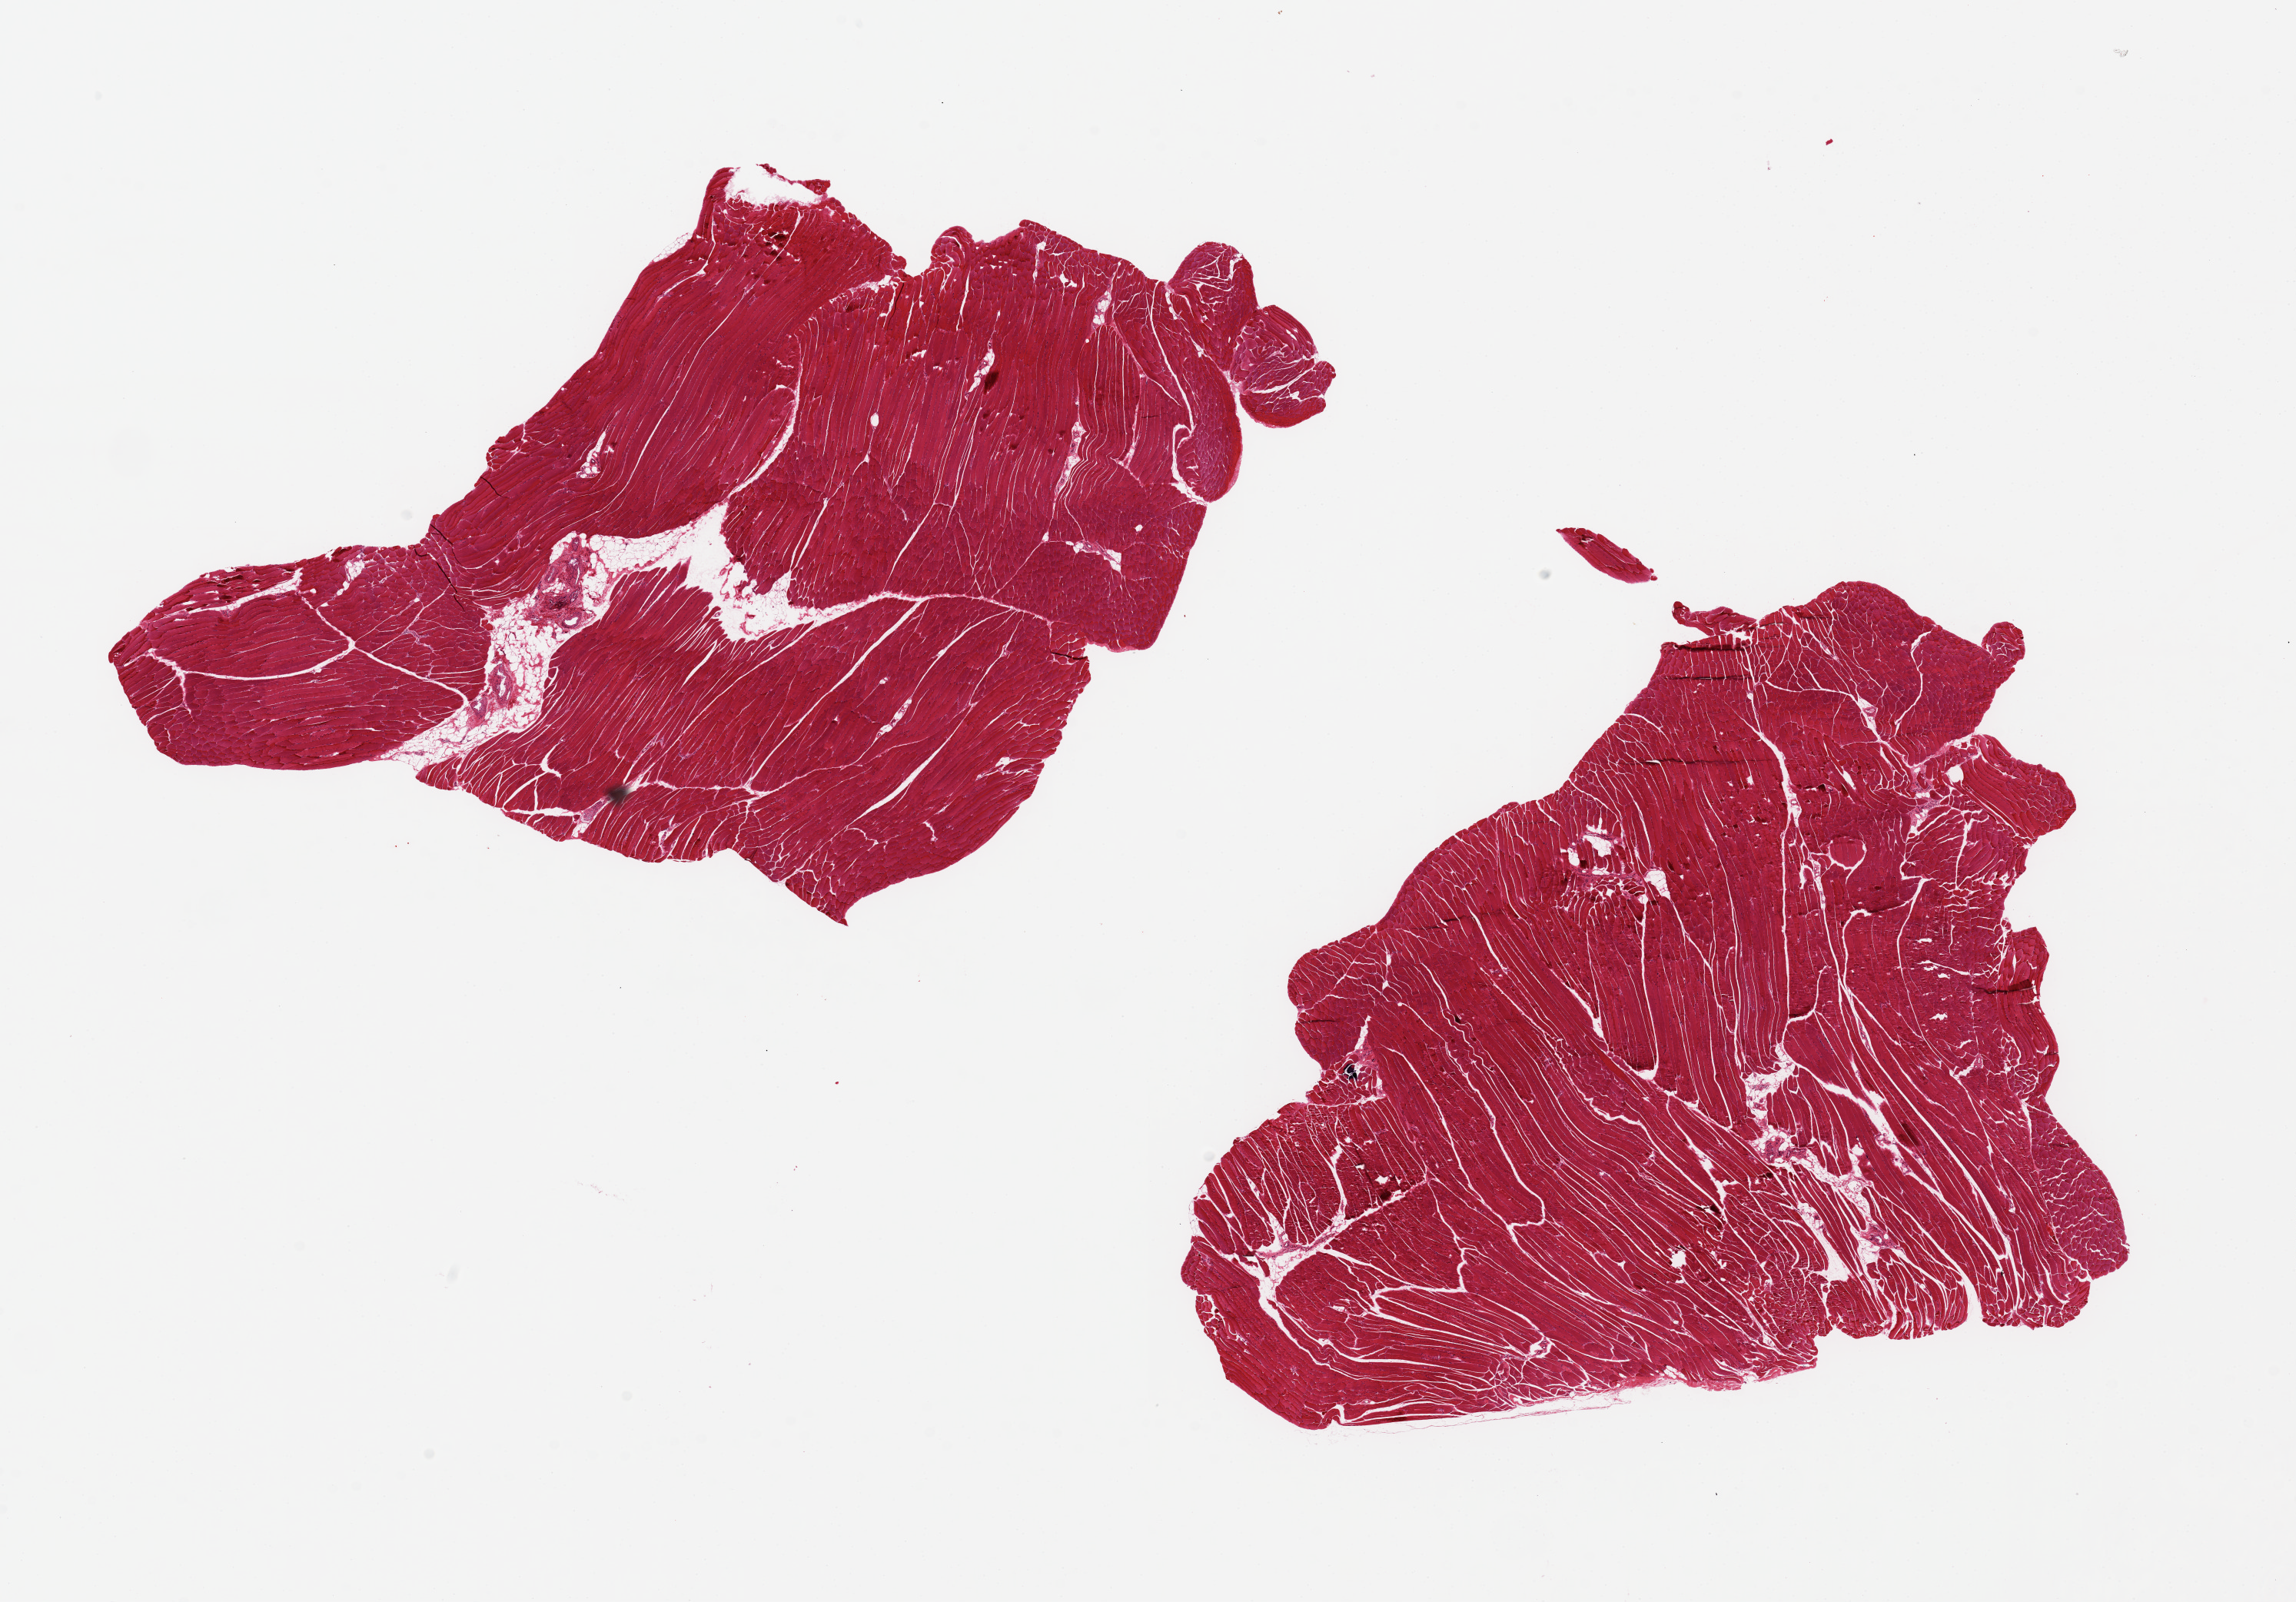
H&E whole-slide image, brightfield, a low-resolution overview of the entire scanned area, about 23.6 x 16.5 mm; PAXgene-fixed paraffin-embedded (PFPE) section; section of skeletal muscle (target tissue); donor tissue sample. Donor: male.
Reviewer comment on this tissue sample: 2 pieces ~9x7mm, minimal interstitial fat.